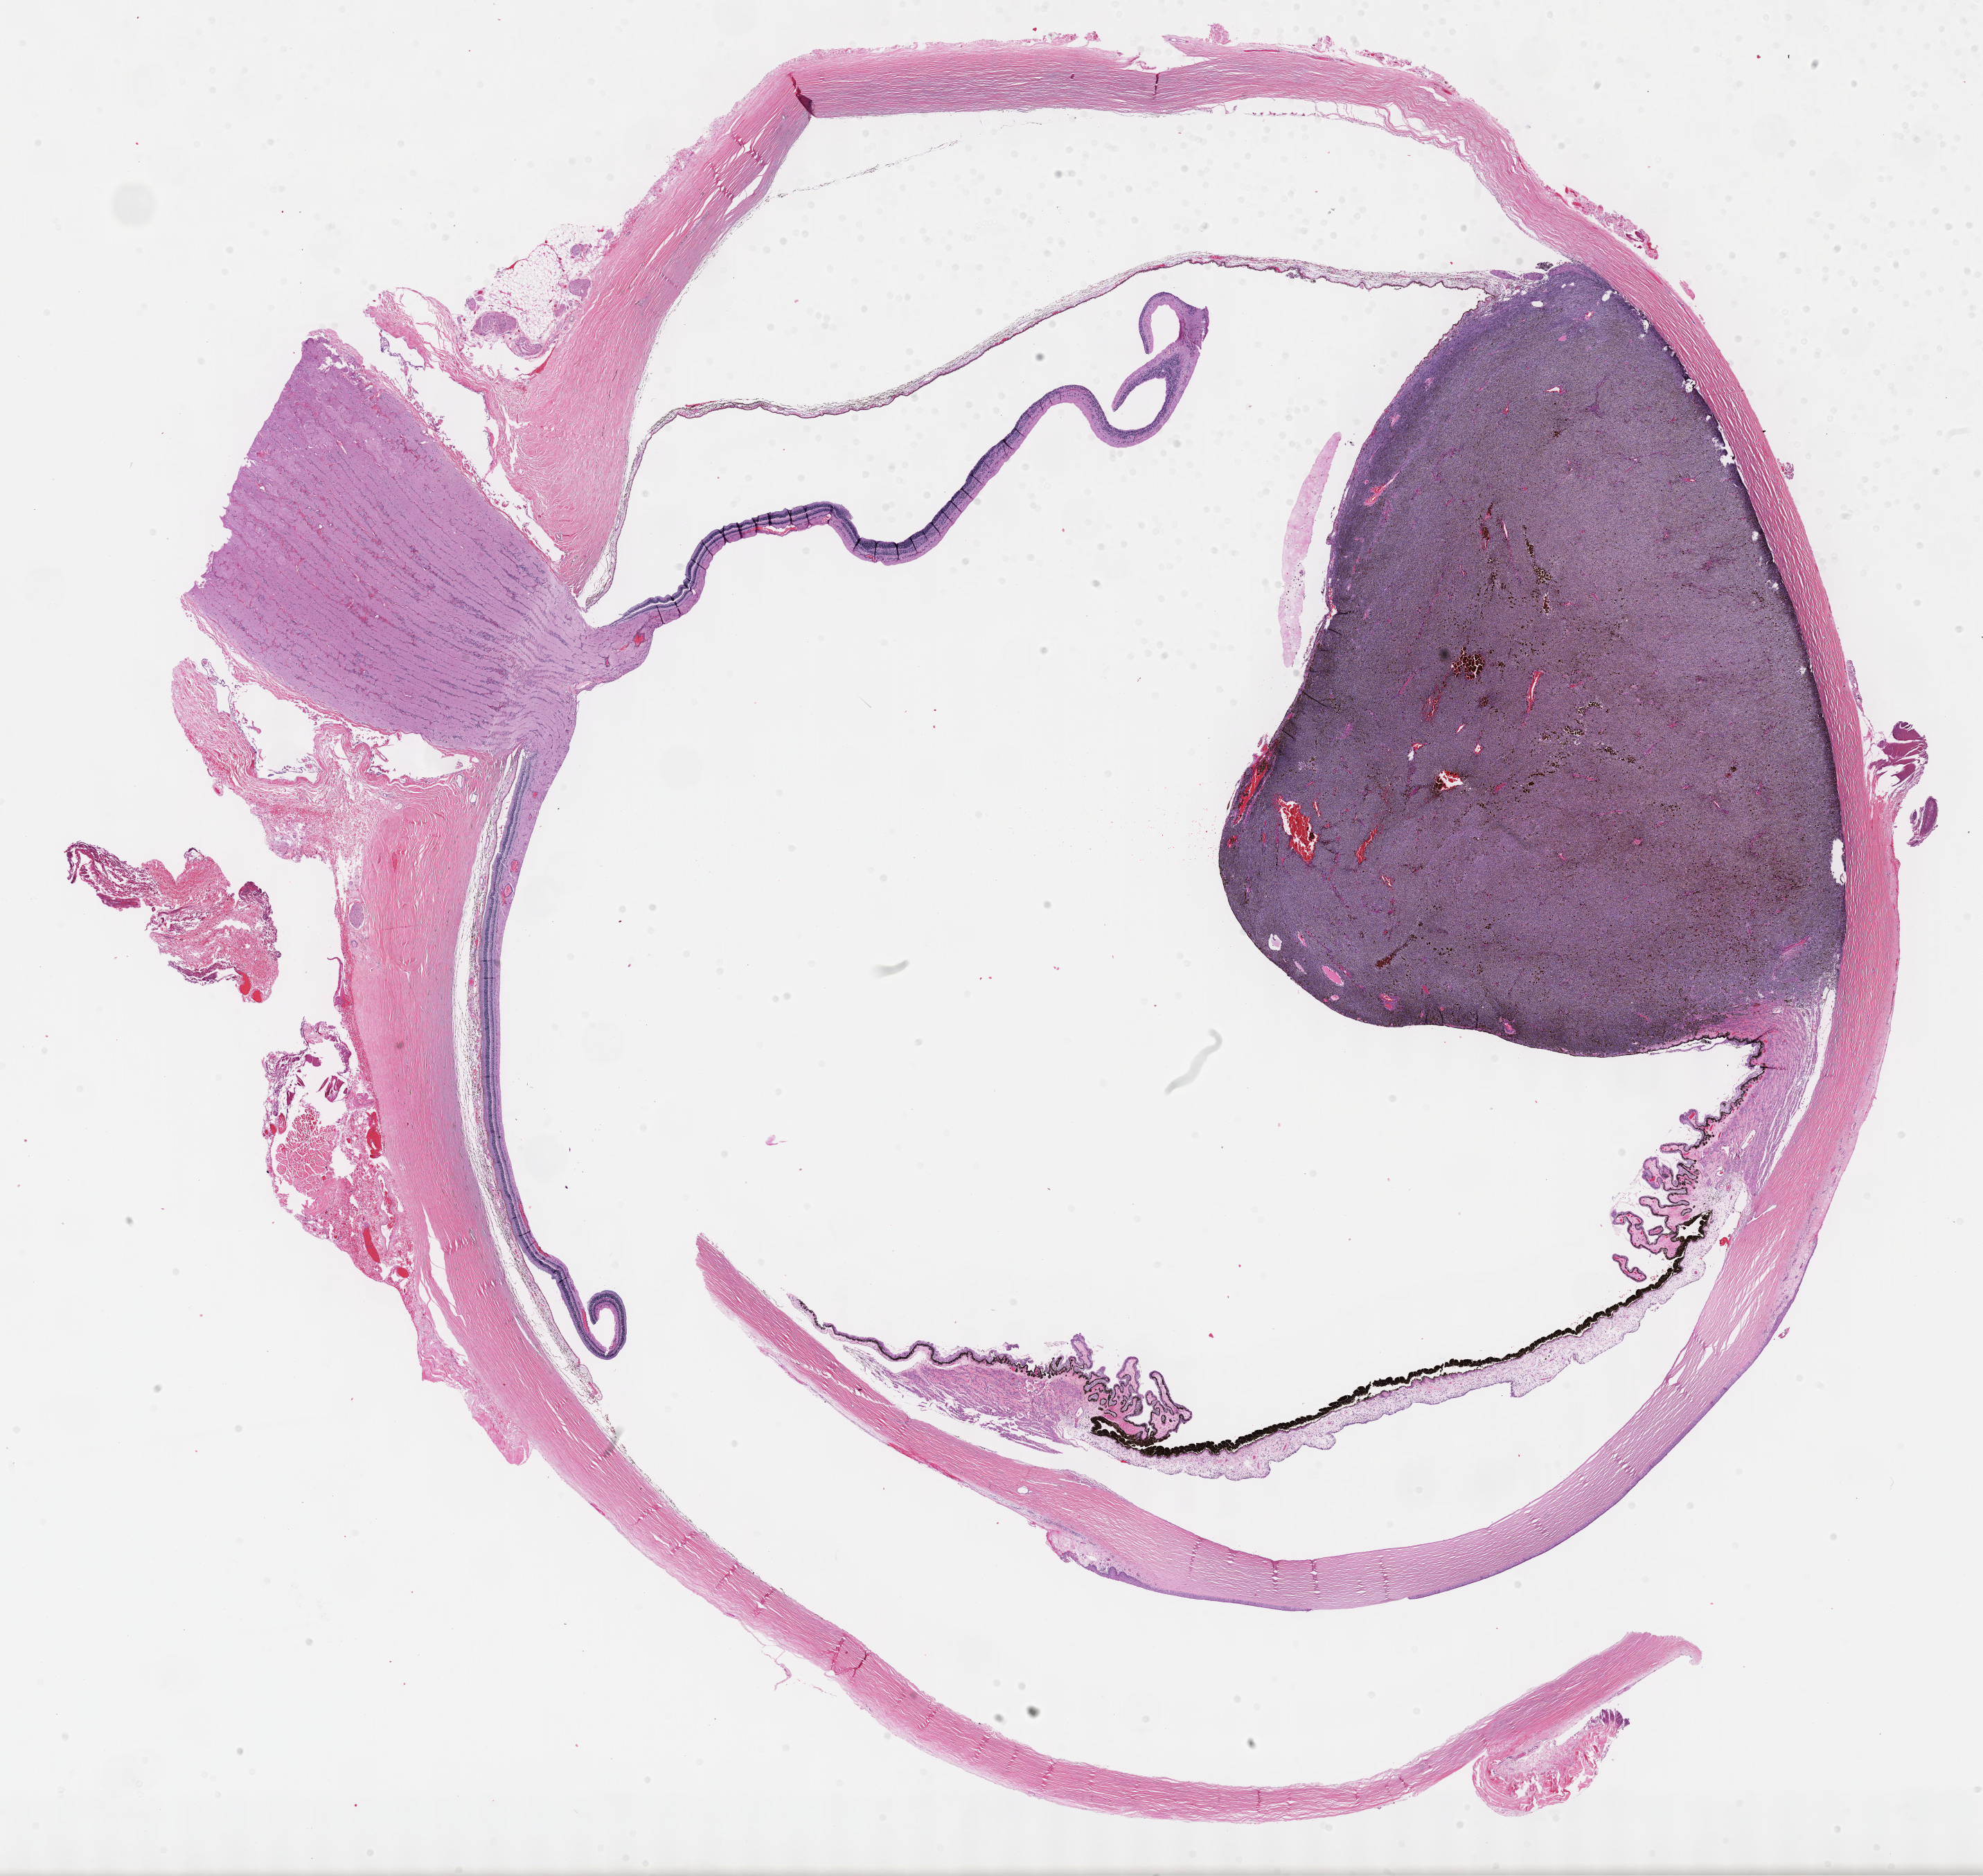
Hematoxylin and eosin (H&E) stained whole-slide image — low-resolution overview of the scanned area, about 23.2 x 21.9 mm (from a 40x scan); formalin-fixed paraffin-embedded (FFPE) diagnostic section; primary tumour sample from the uvea. Female, age 50 years at initial diagnosis.
AJCC pathologic stage: IIB (7th edition). Laterality: right. Histologic diagnosis: Spindle cell melanoma, NOS (overlapping lesion of eye and adnexa).